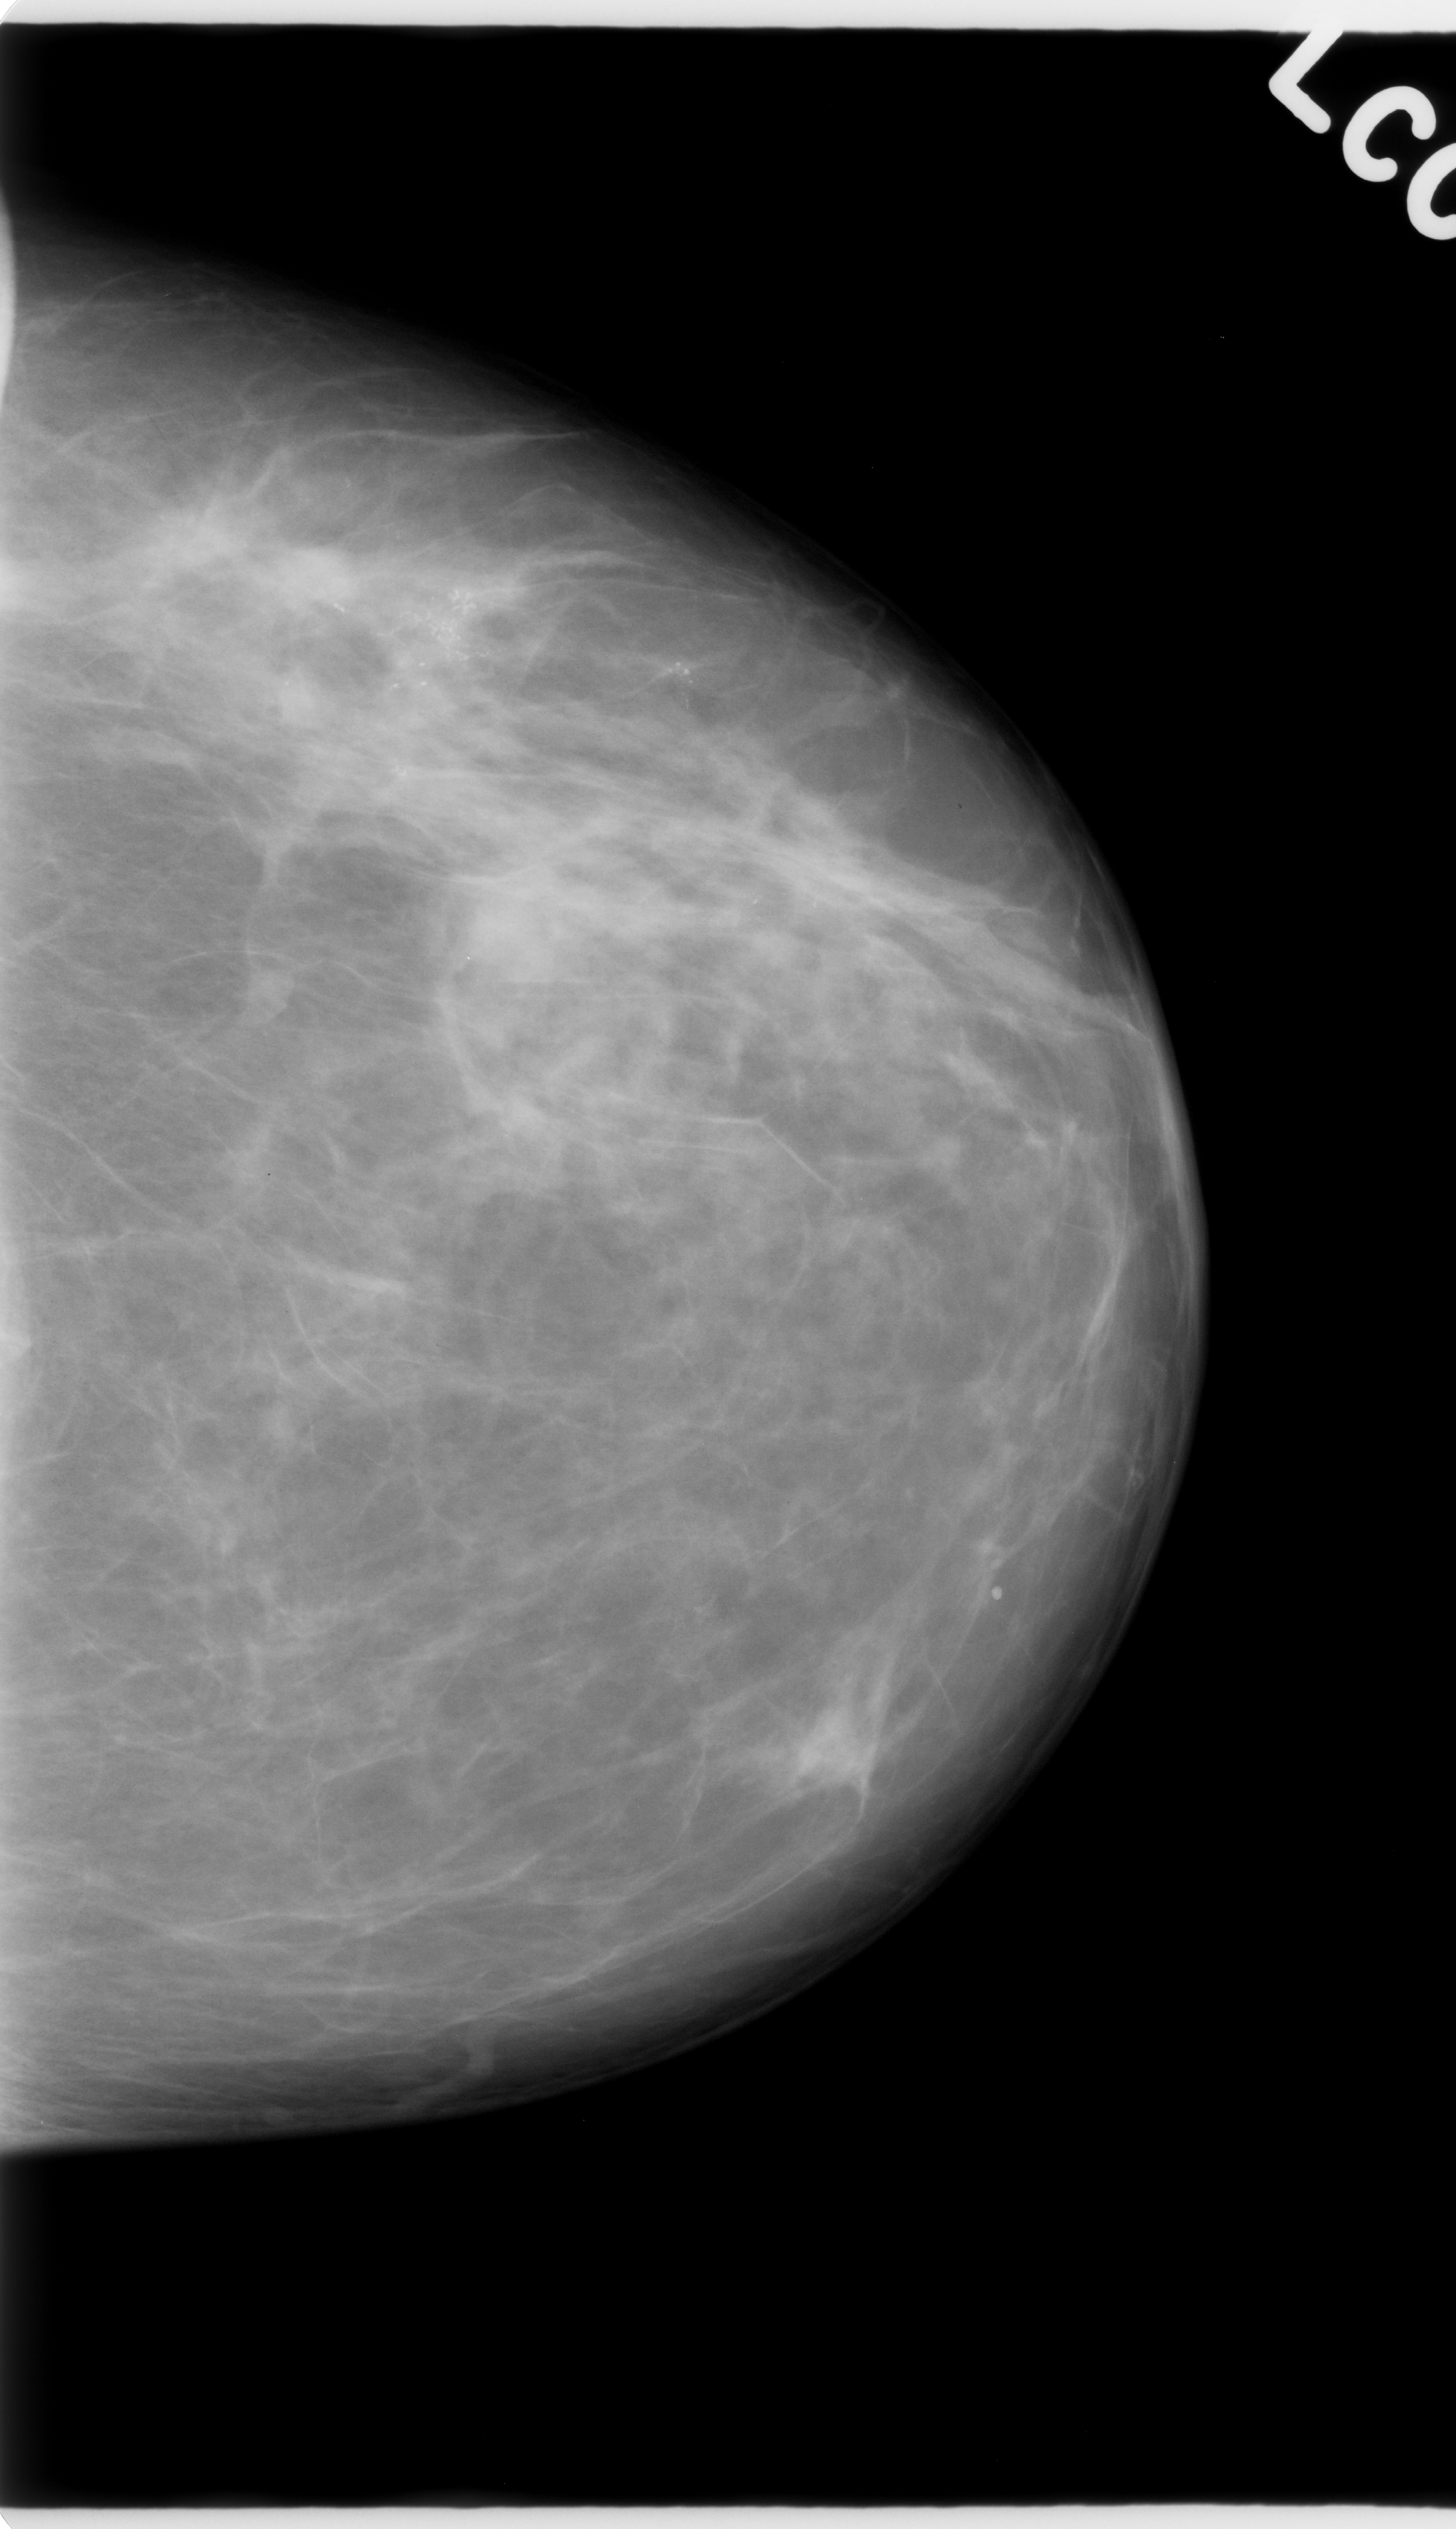
Scanned film-screen mammogram; left breast; CC view; 1456 × 2529 image matrix.
Expert-marked regions of interest on this image (one box per marked abnormality):
- Finding 1 of 2: calcifications, morphology pleomorphic, distribution clustered; BI-RADS assessment category 5; subtlety rating 5 on a 1 (subtle) to 5 (obvious) scale; pathology result (as recorded, not read from the image): malignant: box from (x=0, y=465) to (x=587, y=772) px
- Finding 2 of 2: calcifications, morphology pleomorphic, distribution clustered; BI-RADS assessment category 5; pathology result (as recorded, not read from the image): malignant: (x=594, y=594)–(x=772, y=781)